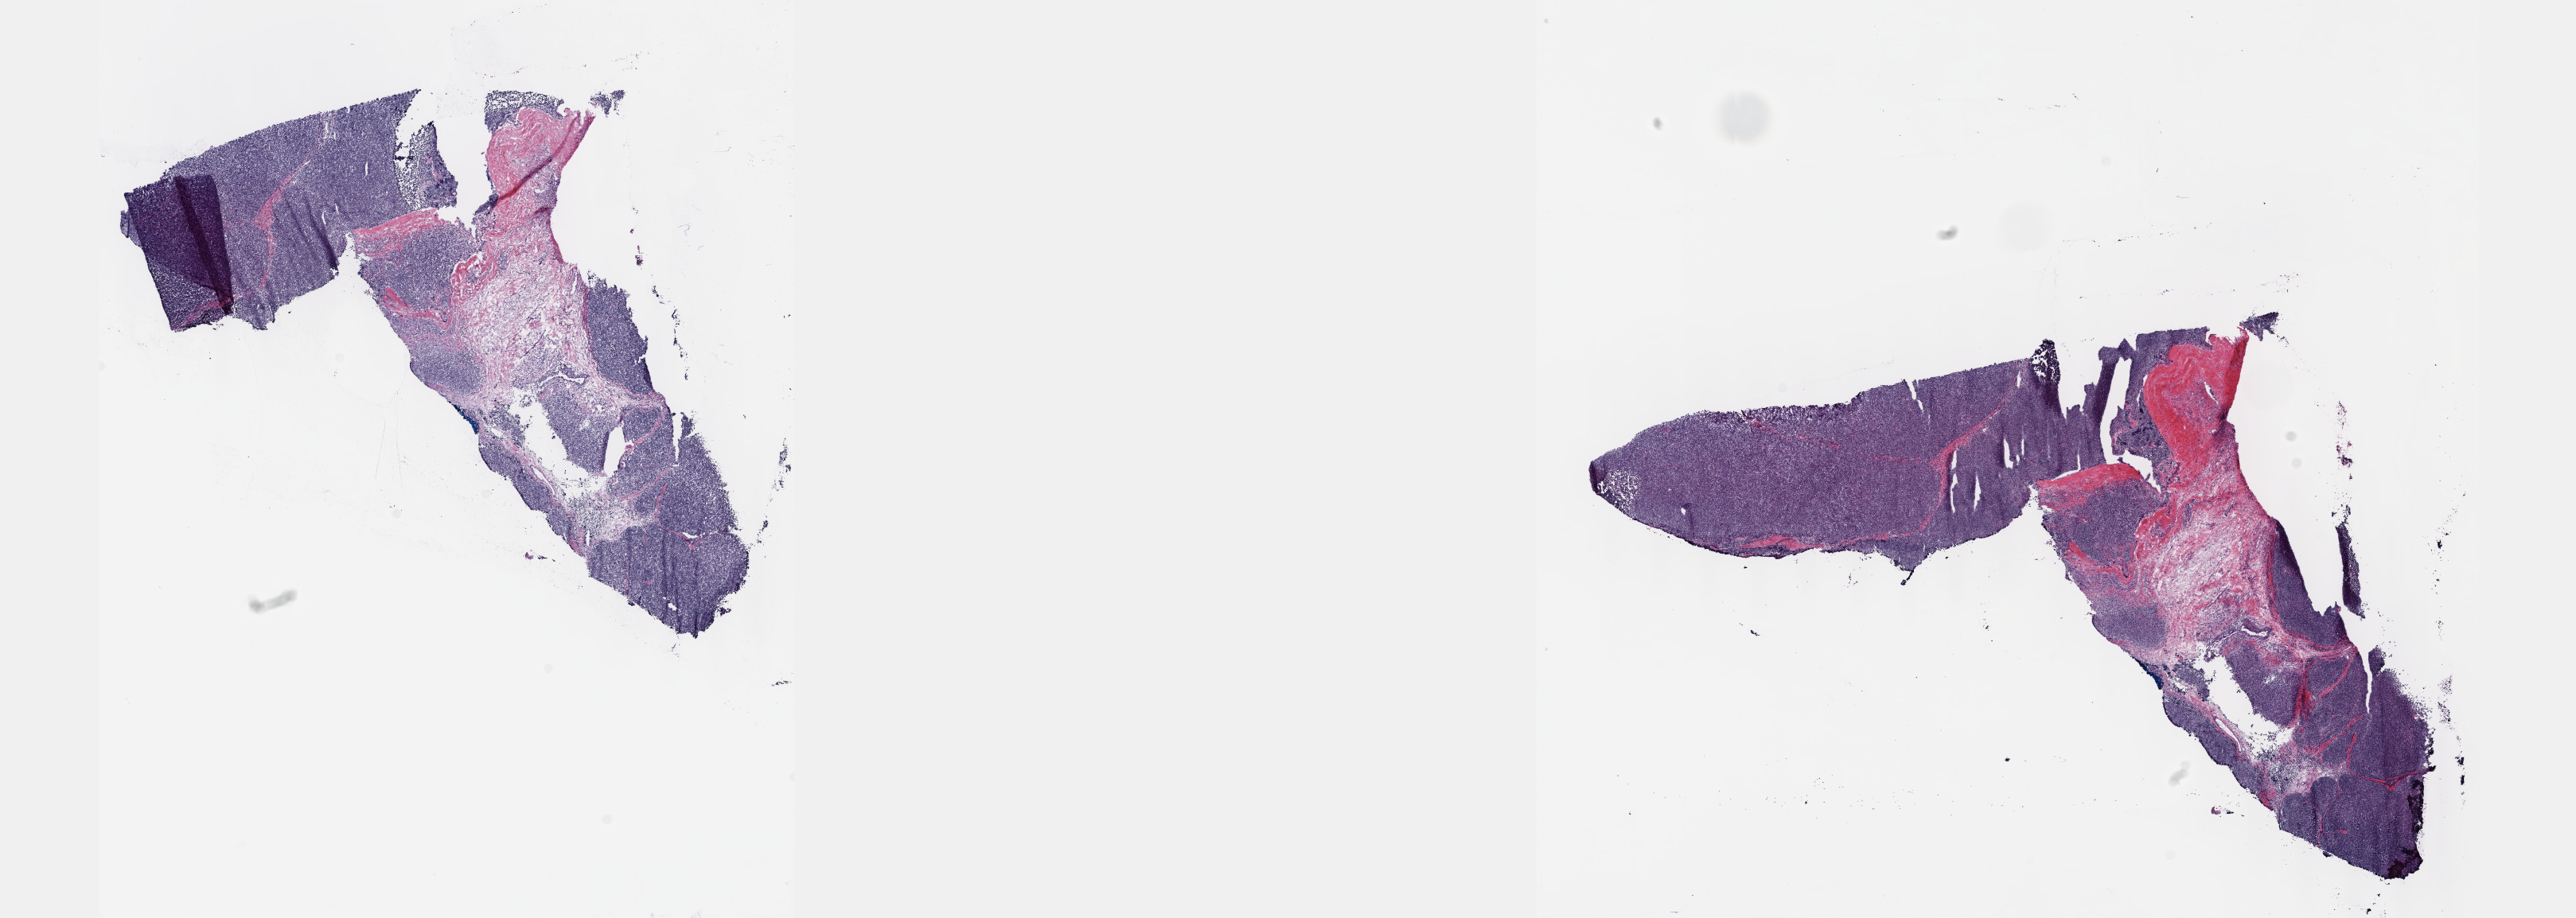
Hematoxylin and eosin (H&E) stained whole-slide image, low-resolution overview of the scanned area, about 26.2 x 9.3 mm. Frozen section. Thymus, primary tumour sample. Female, age 54 years at initial diagnosis. Slide review estimates, as recorded: tumour cells 100%, tumour nuclei 80%.
Pathologic diagnosis: Thymoma, type AB, NOS.